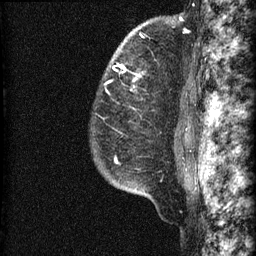
Breast MRI (dynamic contrast-enhanced), one sagittal slice. Slice 52 of 60 in the series (ordered by position). Dynamic contrast-enhanced series, image 2 of 3 at this slice position (ordered by acquisition). 1.5 T. TE 4.2 ms, TR 22.7 ms. 256 × 256 image matrix. Patient: female, 48 years. Case-level facts recorded for this patient, not image findings: setting: breast cancer imaged before/during neoadjuvant chemotherapy; receptor status: triple-negative.
Structures marked on this image (semi-automatic segmentation, software-assisted and operator-edited):
- analysis volume of interest (the breast-tissue region the enhancement analysis was run in; not a lesion): bounding box <89,23,186,202> (left, top, right, bottom; pixels)
- tumour enhancement mask (voxels above the 90 % enhancement threshold inside the analysis volume of interest): <104,63,139,163>